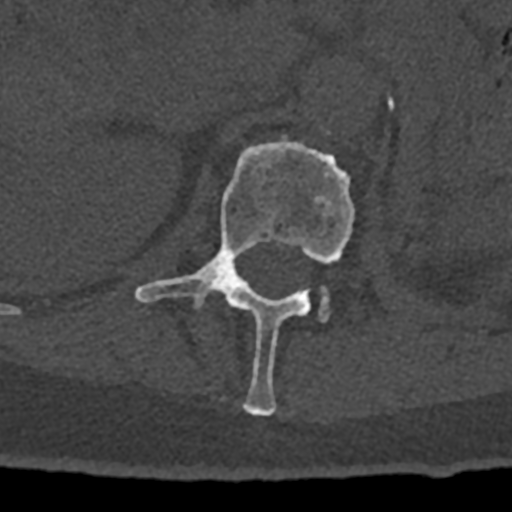
CT including the spine, one axial slice. Slice 428 of 797 in the series (ordered by position). Reconstruction kernel Br40s/3. 120 kVp. Bone window (W 1800 / L 400 HU). 512 × 512 image matrix, field of view 160 × 160 mm. Male patient, age 74 years. From the clinical record (not read from this slice): primary cancer: renal; vertebrae with lytic lesions (as recorded): T10, L1, L2, L3, L4, L5.
Annotated regions visible in this slice (semi-automatically segmented with operator editing):
- L1 vertebra: box from (x=135, y=138) to (x=355, y=416) px
- L2 vertebra: (x=319, y=293)–(x=330, y=322)